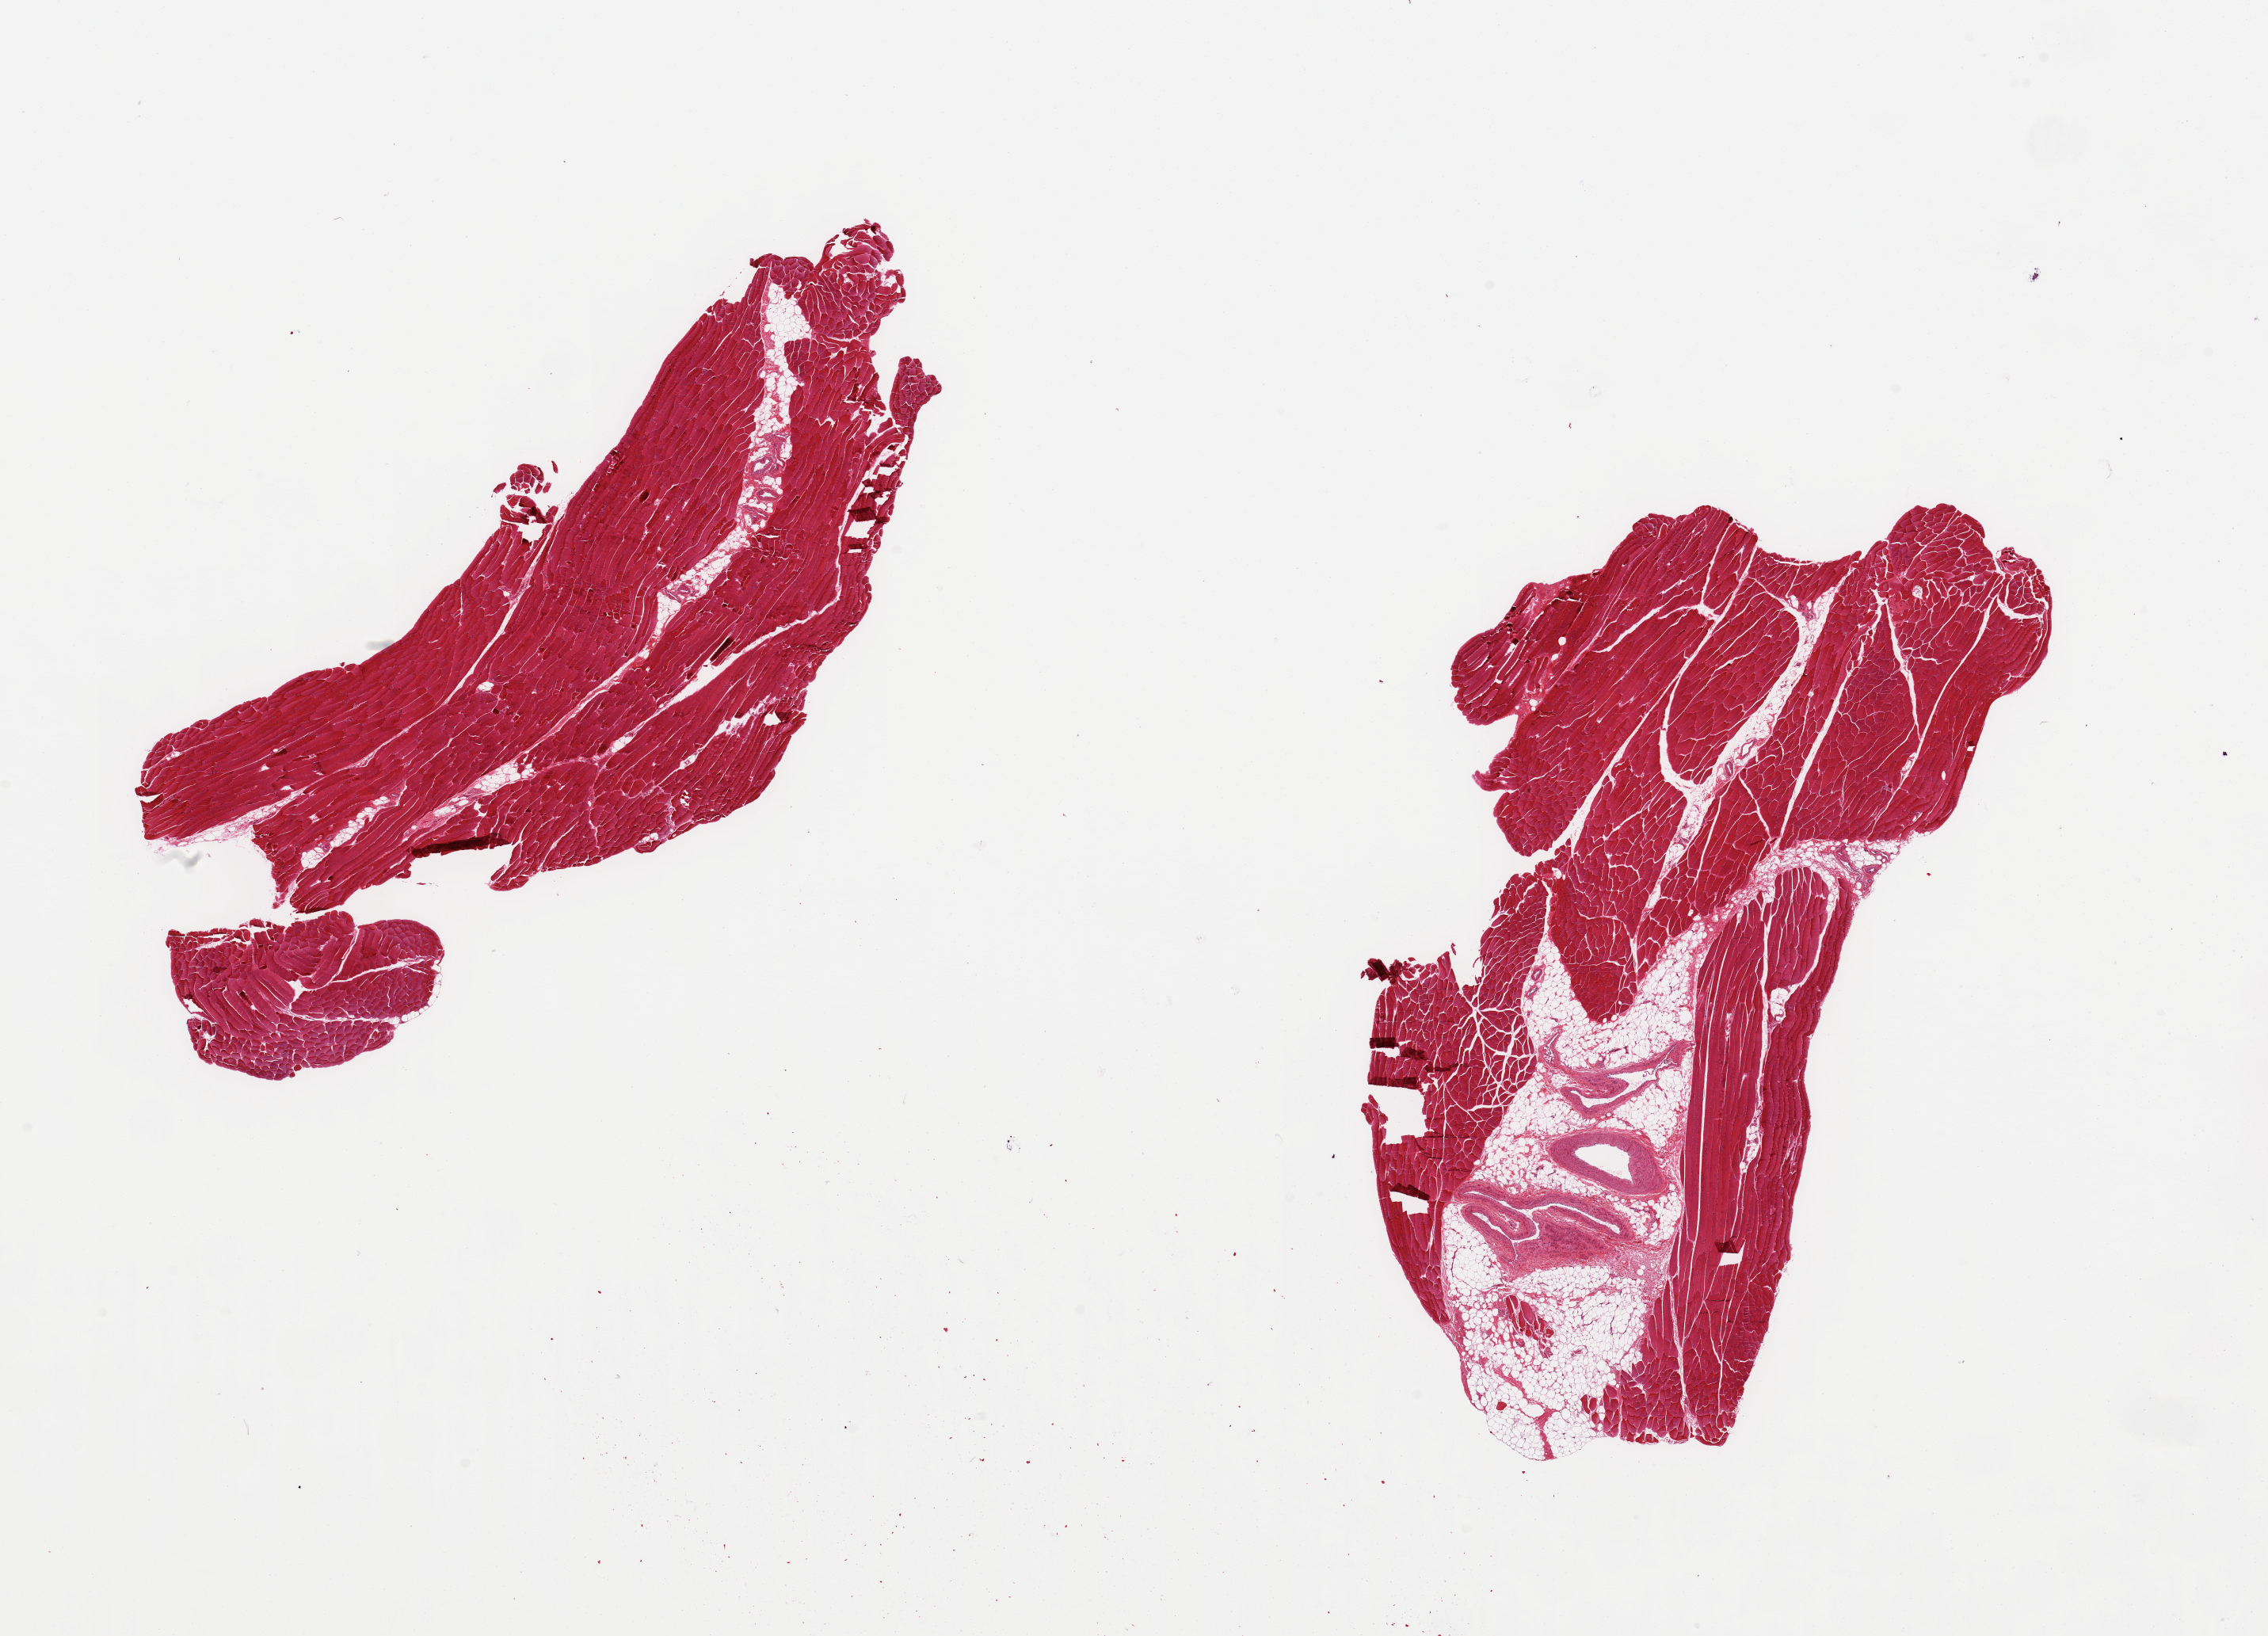
Whole-slide image, H&E stain, low-resolution overview of the scanned area, about 22.6 x 16.3 mm. PAXgene-fixed, paraffin-embedded tissue. Target tissue: skeletal muscle. Donor tissue sample.
* pathologist's review note for this sample: 2 pieces; 1 with 30% fat and vascular content